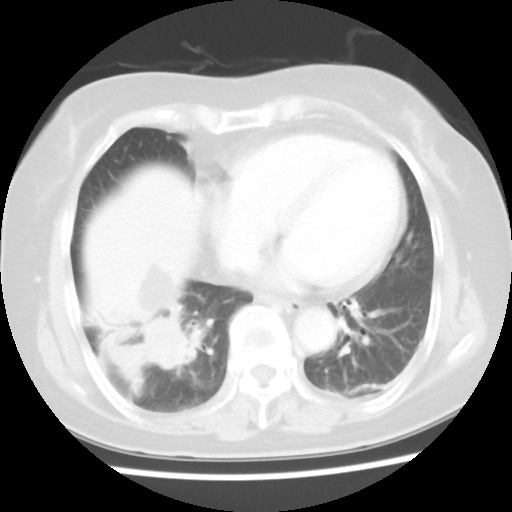
Chest CT, one axial slice; position 15 of 45 along the scan axis; reconstruction kernel STANDARD; 120 kVp; lung window (W 1500 / L -600 HU); 5 mm slice thickness; 512 × 512 image matrix. Female patient, age 65 years. From the clinical record (not read from this slice): clinical TNM (as recorded): T2 N3 M0.
Annotated regions visible in this slice (bounding box drawn by a radiologist):
- lung tumour (recorded histology: adenocarcinoma): bounding box <139,307,195,374> (left, top, right, bottom; pixels)